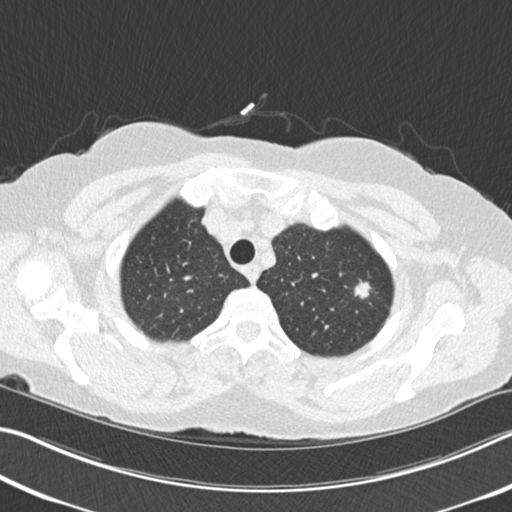
Low-dose screening chest CT, one axial slice; slice 194 of 225 in the series (ordered by position); 120 kVp; lung window (W 1500 / L -600 HU); 512 × 512 image matrix.
Annotated regions visible in this slice (outlined manually by an expert reader):
- lesion 1 (tumor): bounding box (x1, y1, x2, y2) in pixels: (354, 280, 371, 299)